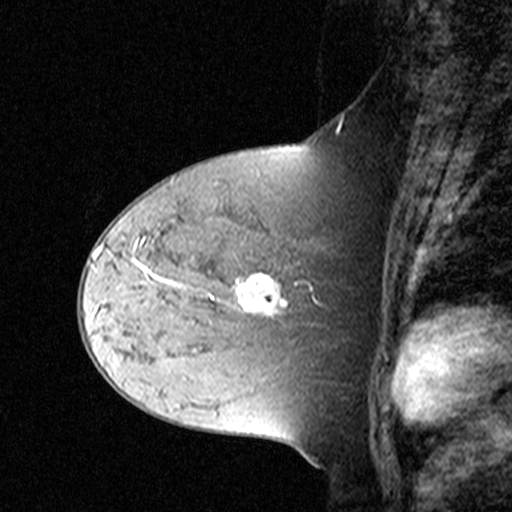
Breast MRI (dynamic contrast-enhanced), one sagittal slice. Dynamic contrast-enhanced study with each time point stored as its own series, time point 2 of 3 at this slice position (early post-contrast, ordered by acquisition time). 1.5 T. TE 4.5 ms, TR 11 ms. 3 mm slice thickness. 512 × 512 image matrix. Patient: female, 44 years. From the clinical record (not read from this slice): setting: breast cancer imaged before/during neoadjuvant chemotherapy; receptor status: triple-negative.
Outlined on this slice (semi-automatically segmented with operator editing):
- analysis volume of interest (the breast-tissue region the enhancement analysis was run in; not a lesion): bounding box (x1, y1, x2, y2) in pixels: (132, 212, 309, 331)
- tumour enhancement mask (voxels above the 90 % enhancement threshold inside the analysis volume of interest): (137, 261, 287, 315)